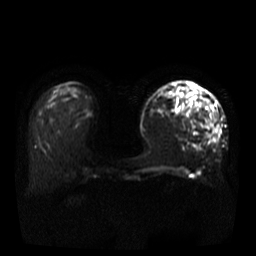
Breast MRI, one axial slice; position 11 of 37 along the scan axis; diffusion-weighted series; image 2 of 4 stored at this slice position (different b-values; order by instance number); 3 T; 5 mm slice thickness; 256 × 256 image matrix, field of view 380 × 380 mm. Female patient.
Structures marked on this image (expert manual segmentation):
- tumour on diffusion-weighted imaging: box from (x=201, y=97) to (x=220, y=142) px